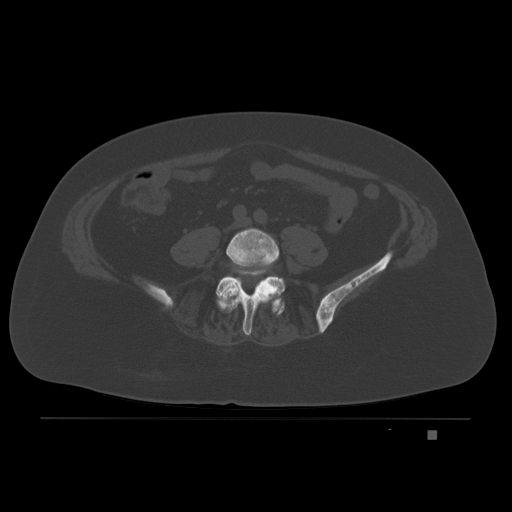
CT including the spine, one axial slice; position 35 of 221 along the scan axis; bone window (W 1800 / L 400 HU); 3 mm slice thickness; 512 × 512 image matrix, field of view 474 × 474 mm. Patient: female, 63 years. Case-level facts recorded for this patient, not image findings: primary cancer: breast.
Outlined on this slice (semi-automatically segmented with operator editing):
- L4 vertebra: bounding box <217,227,279,304> (left, top, right, bottom; pixels)
- L5 vertebra: <216,269,286,335>